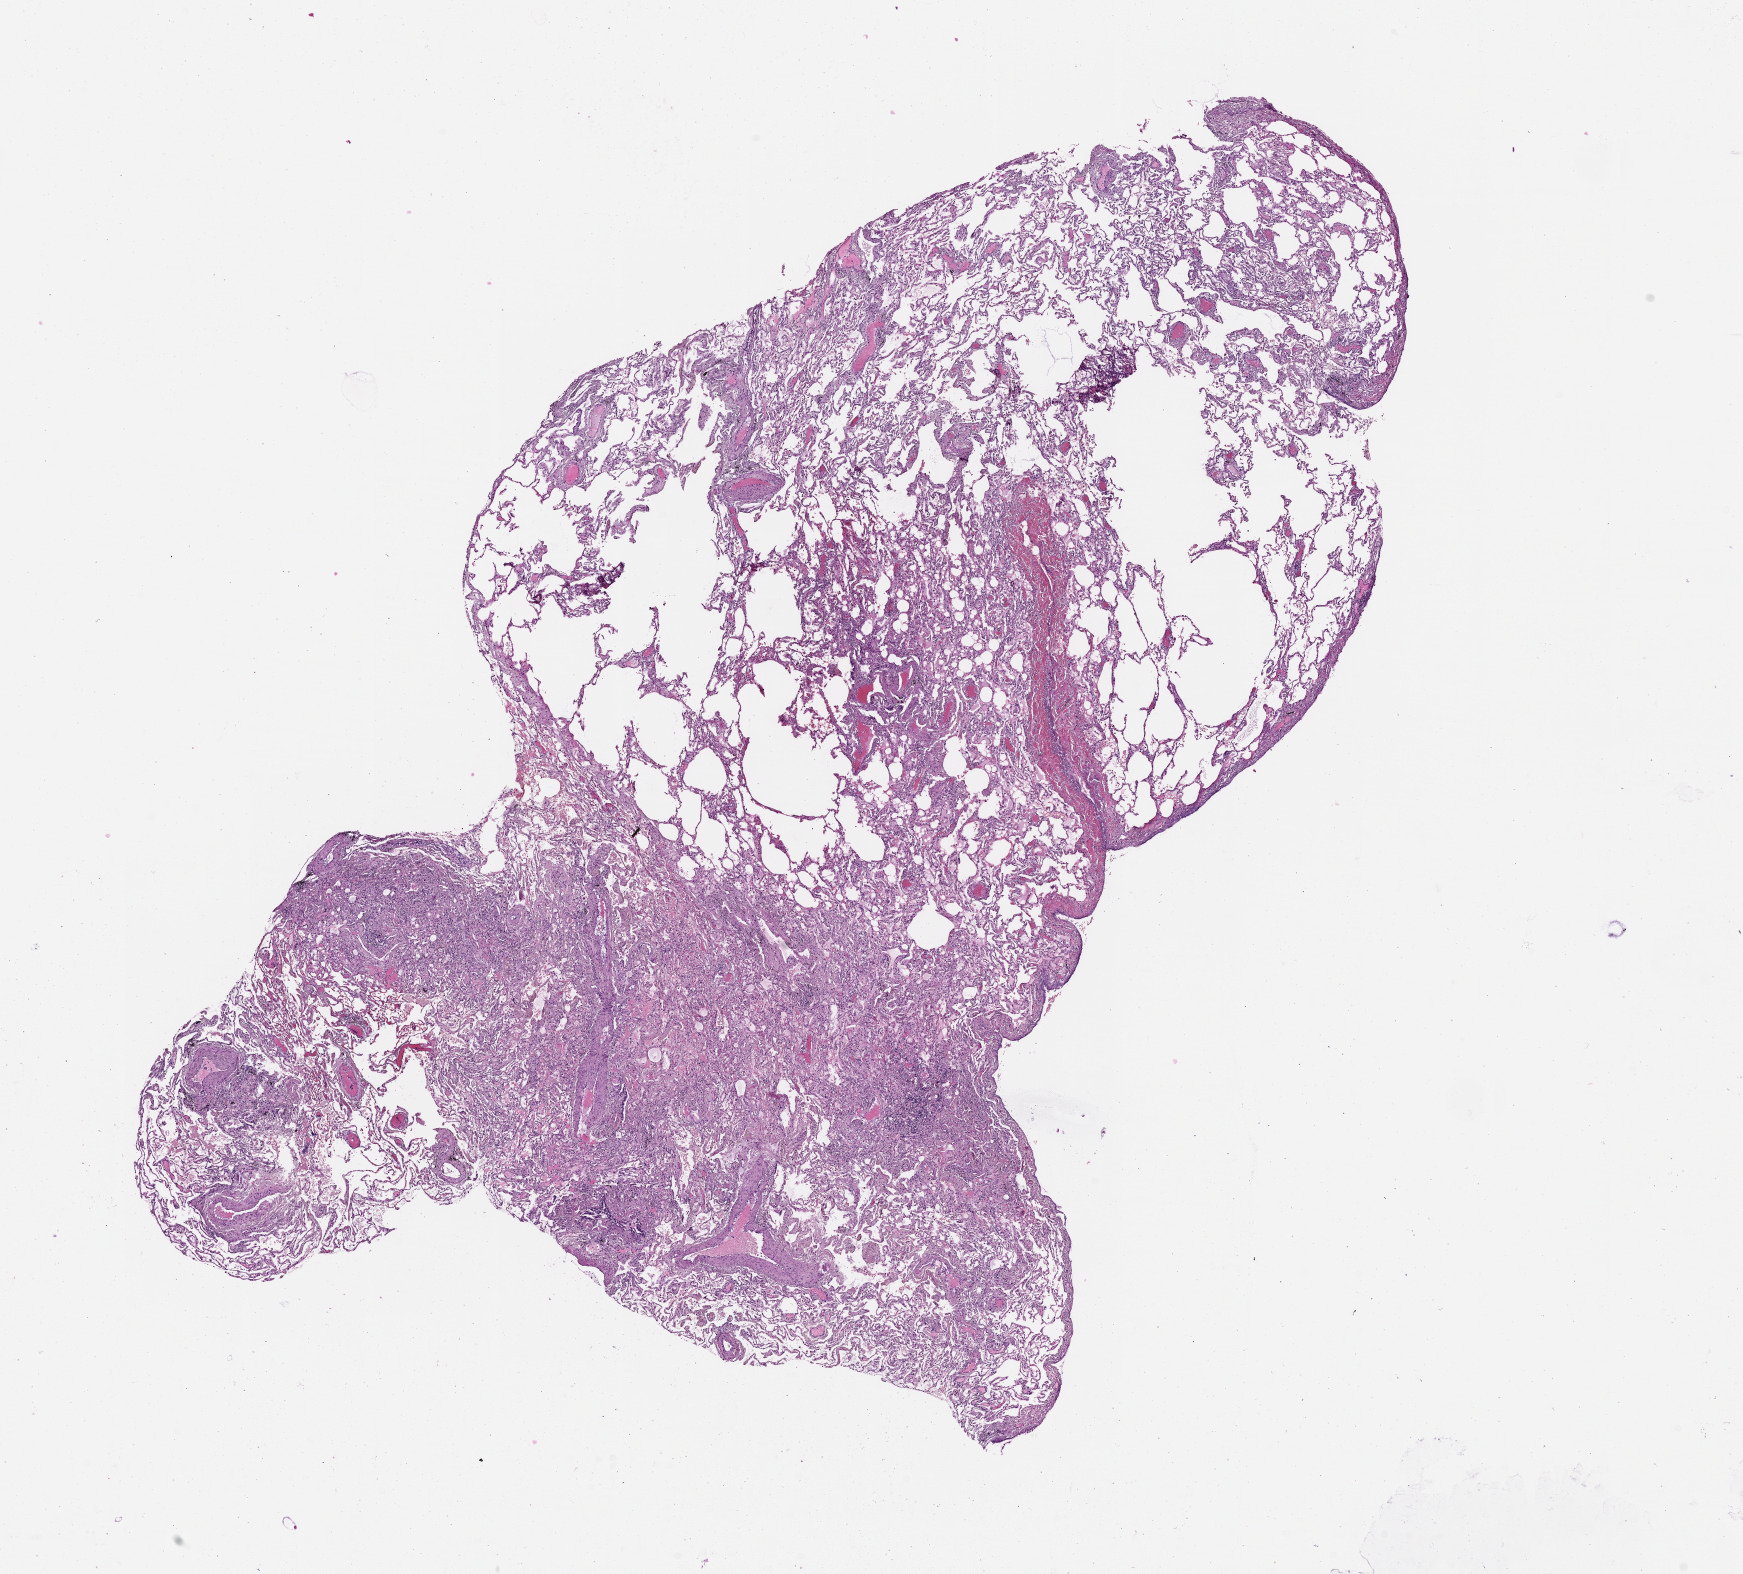
Whole-slide histology image, H&E-stained — whole scanned area (about 14.0 x 12.7 mm, acquisition: 20x scan) shown as a low-resolution overview; lung, tissue type not recorded.
• patient diagnosis (cohort enrolment): squamous cell carcinoma (lung)